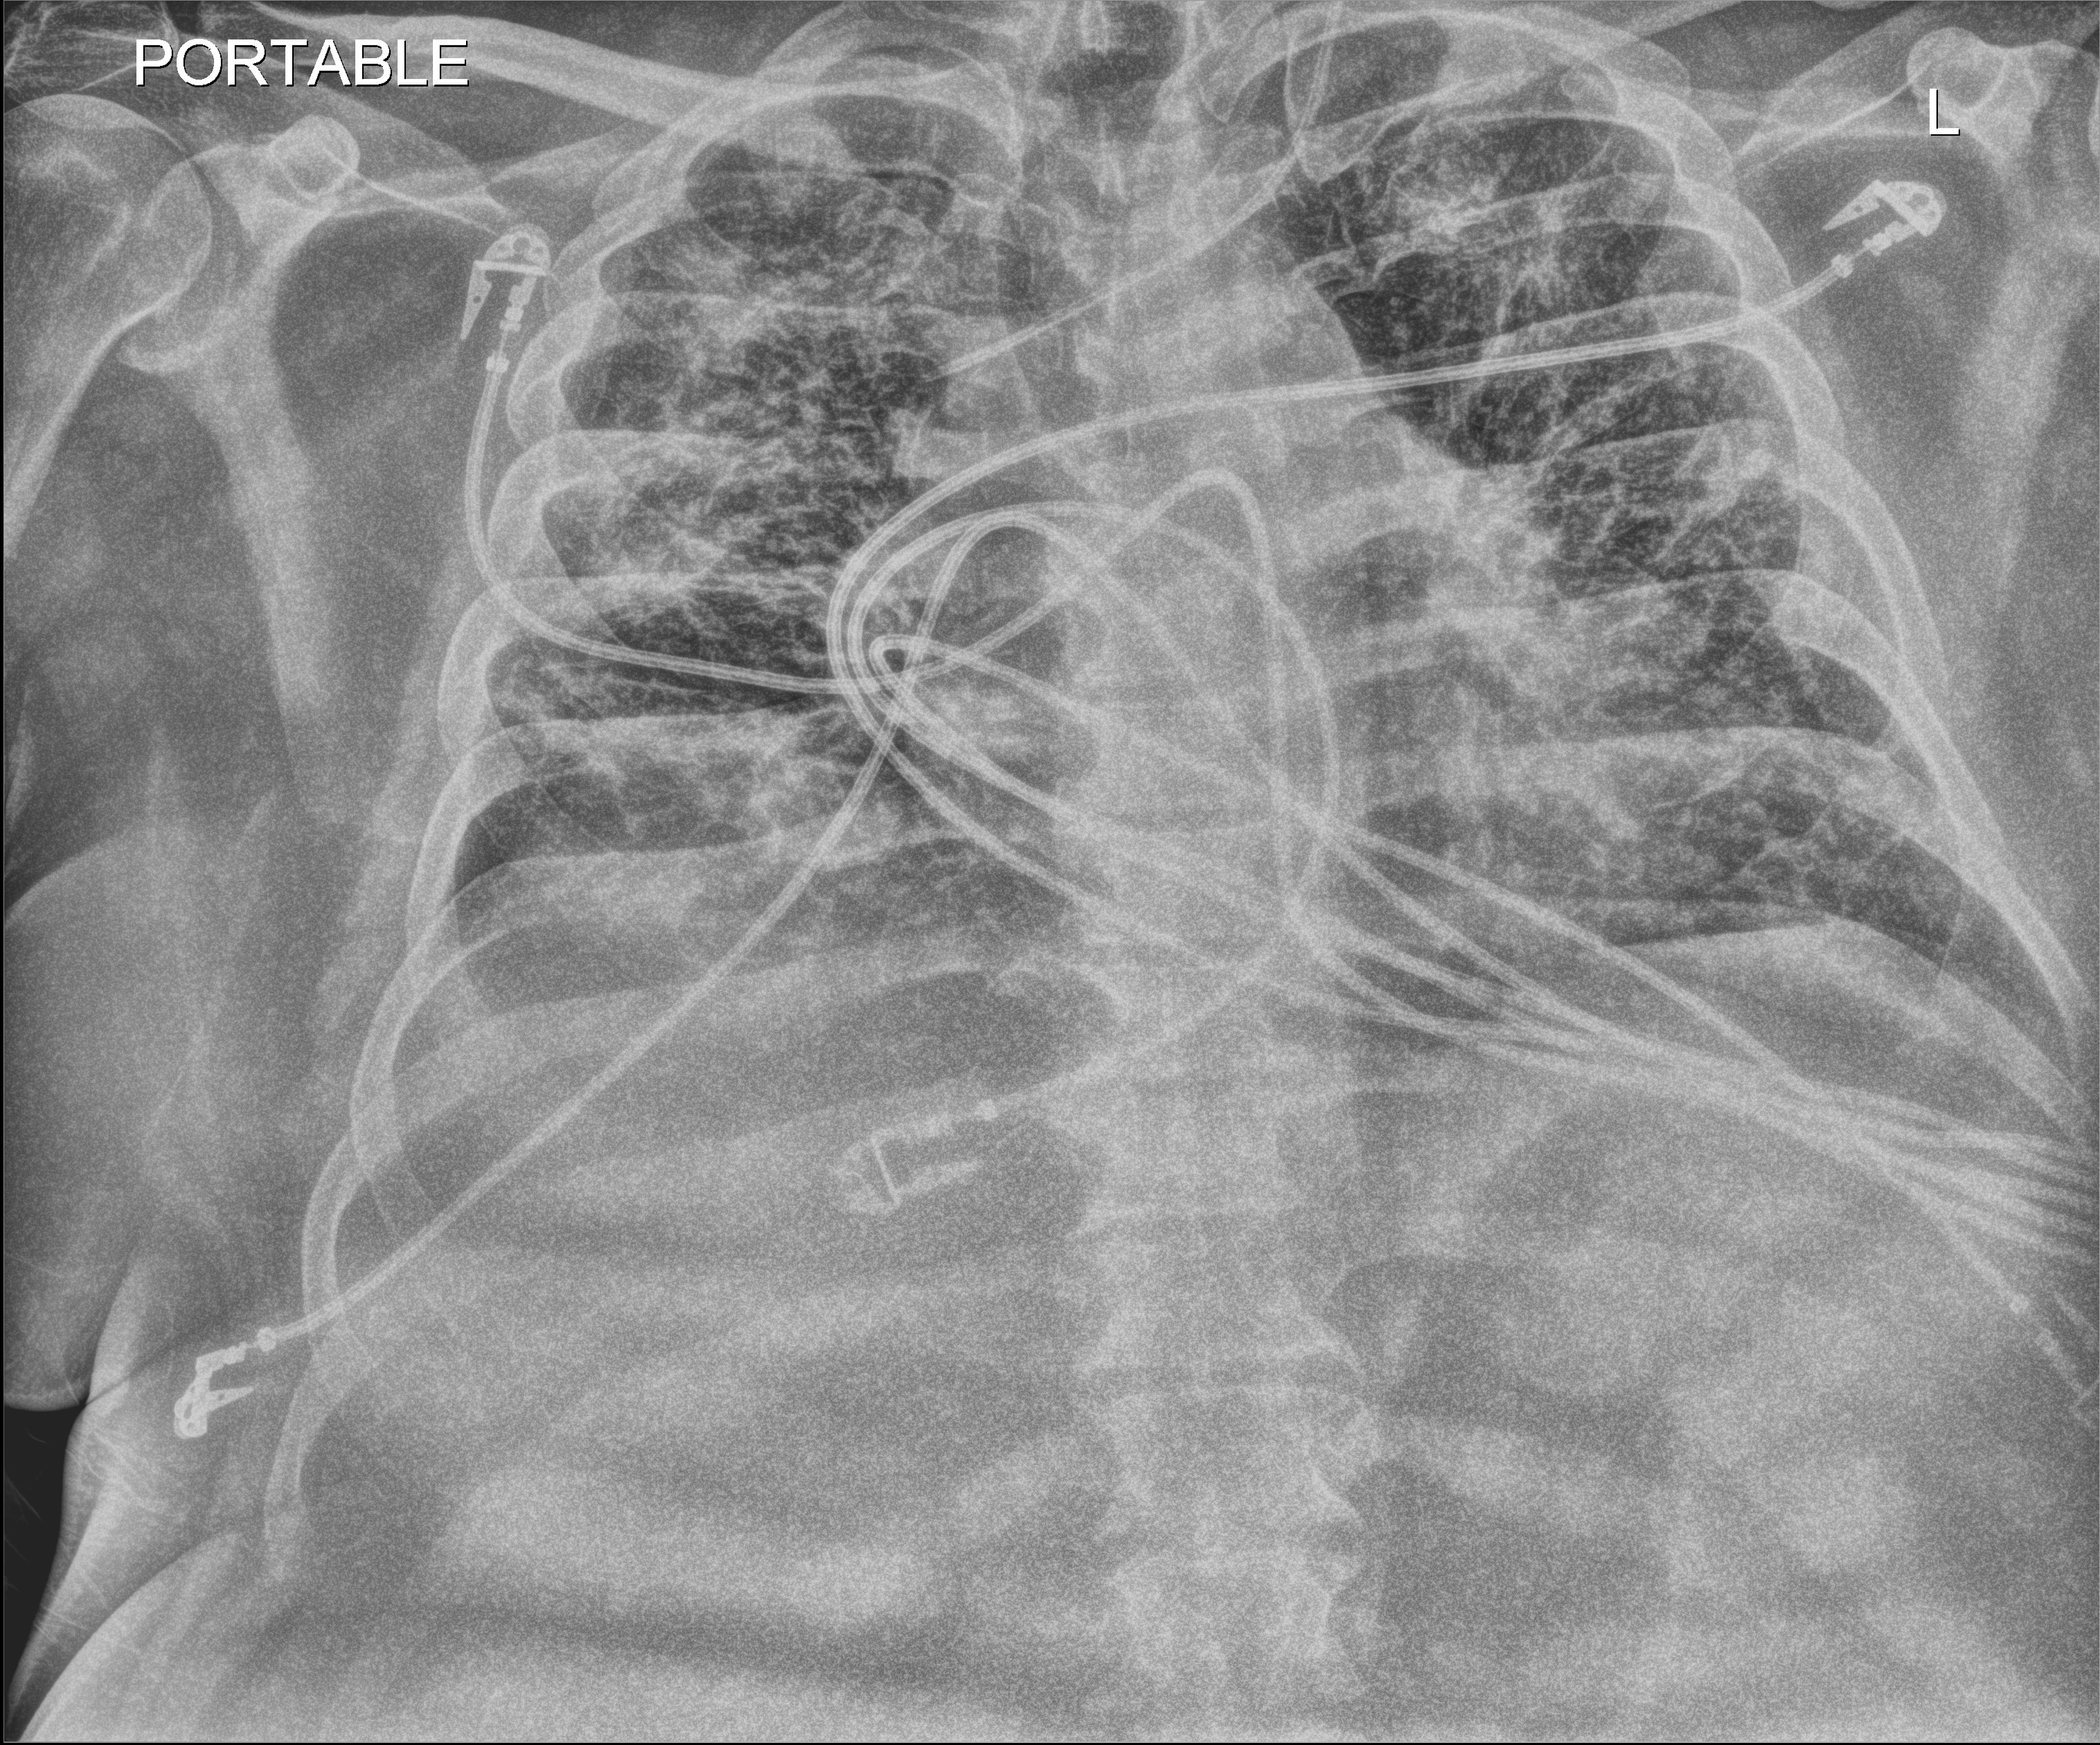
Bedside chest radiograph (digital radiography). Male patient hospitalised with COVID-19, age 18–59 years.
From the hospital-stay record, not from the radiograph (when in the stay this image was taken is not recorded): admitted to intensive care during this hospital stay: yes; mechanically ventilated during this hospital stay: yes.